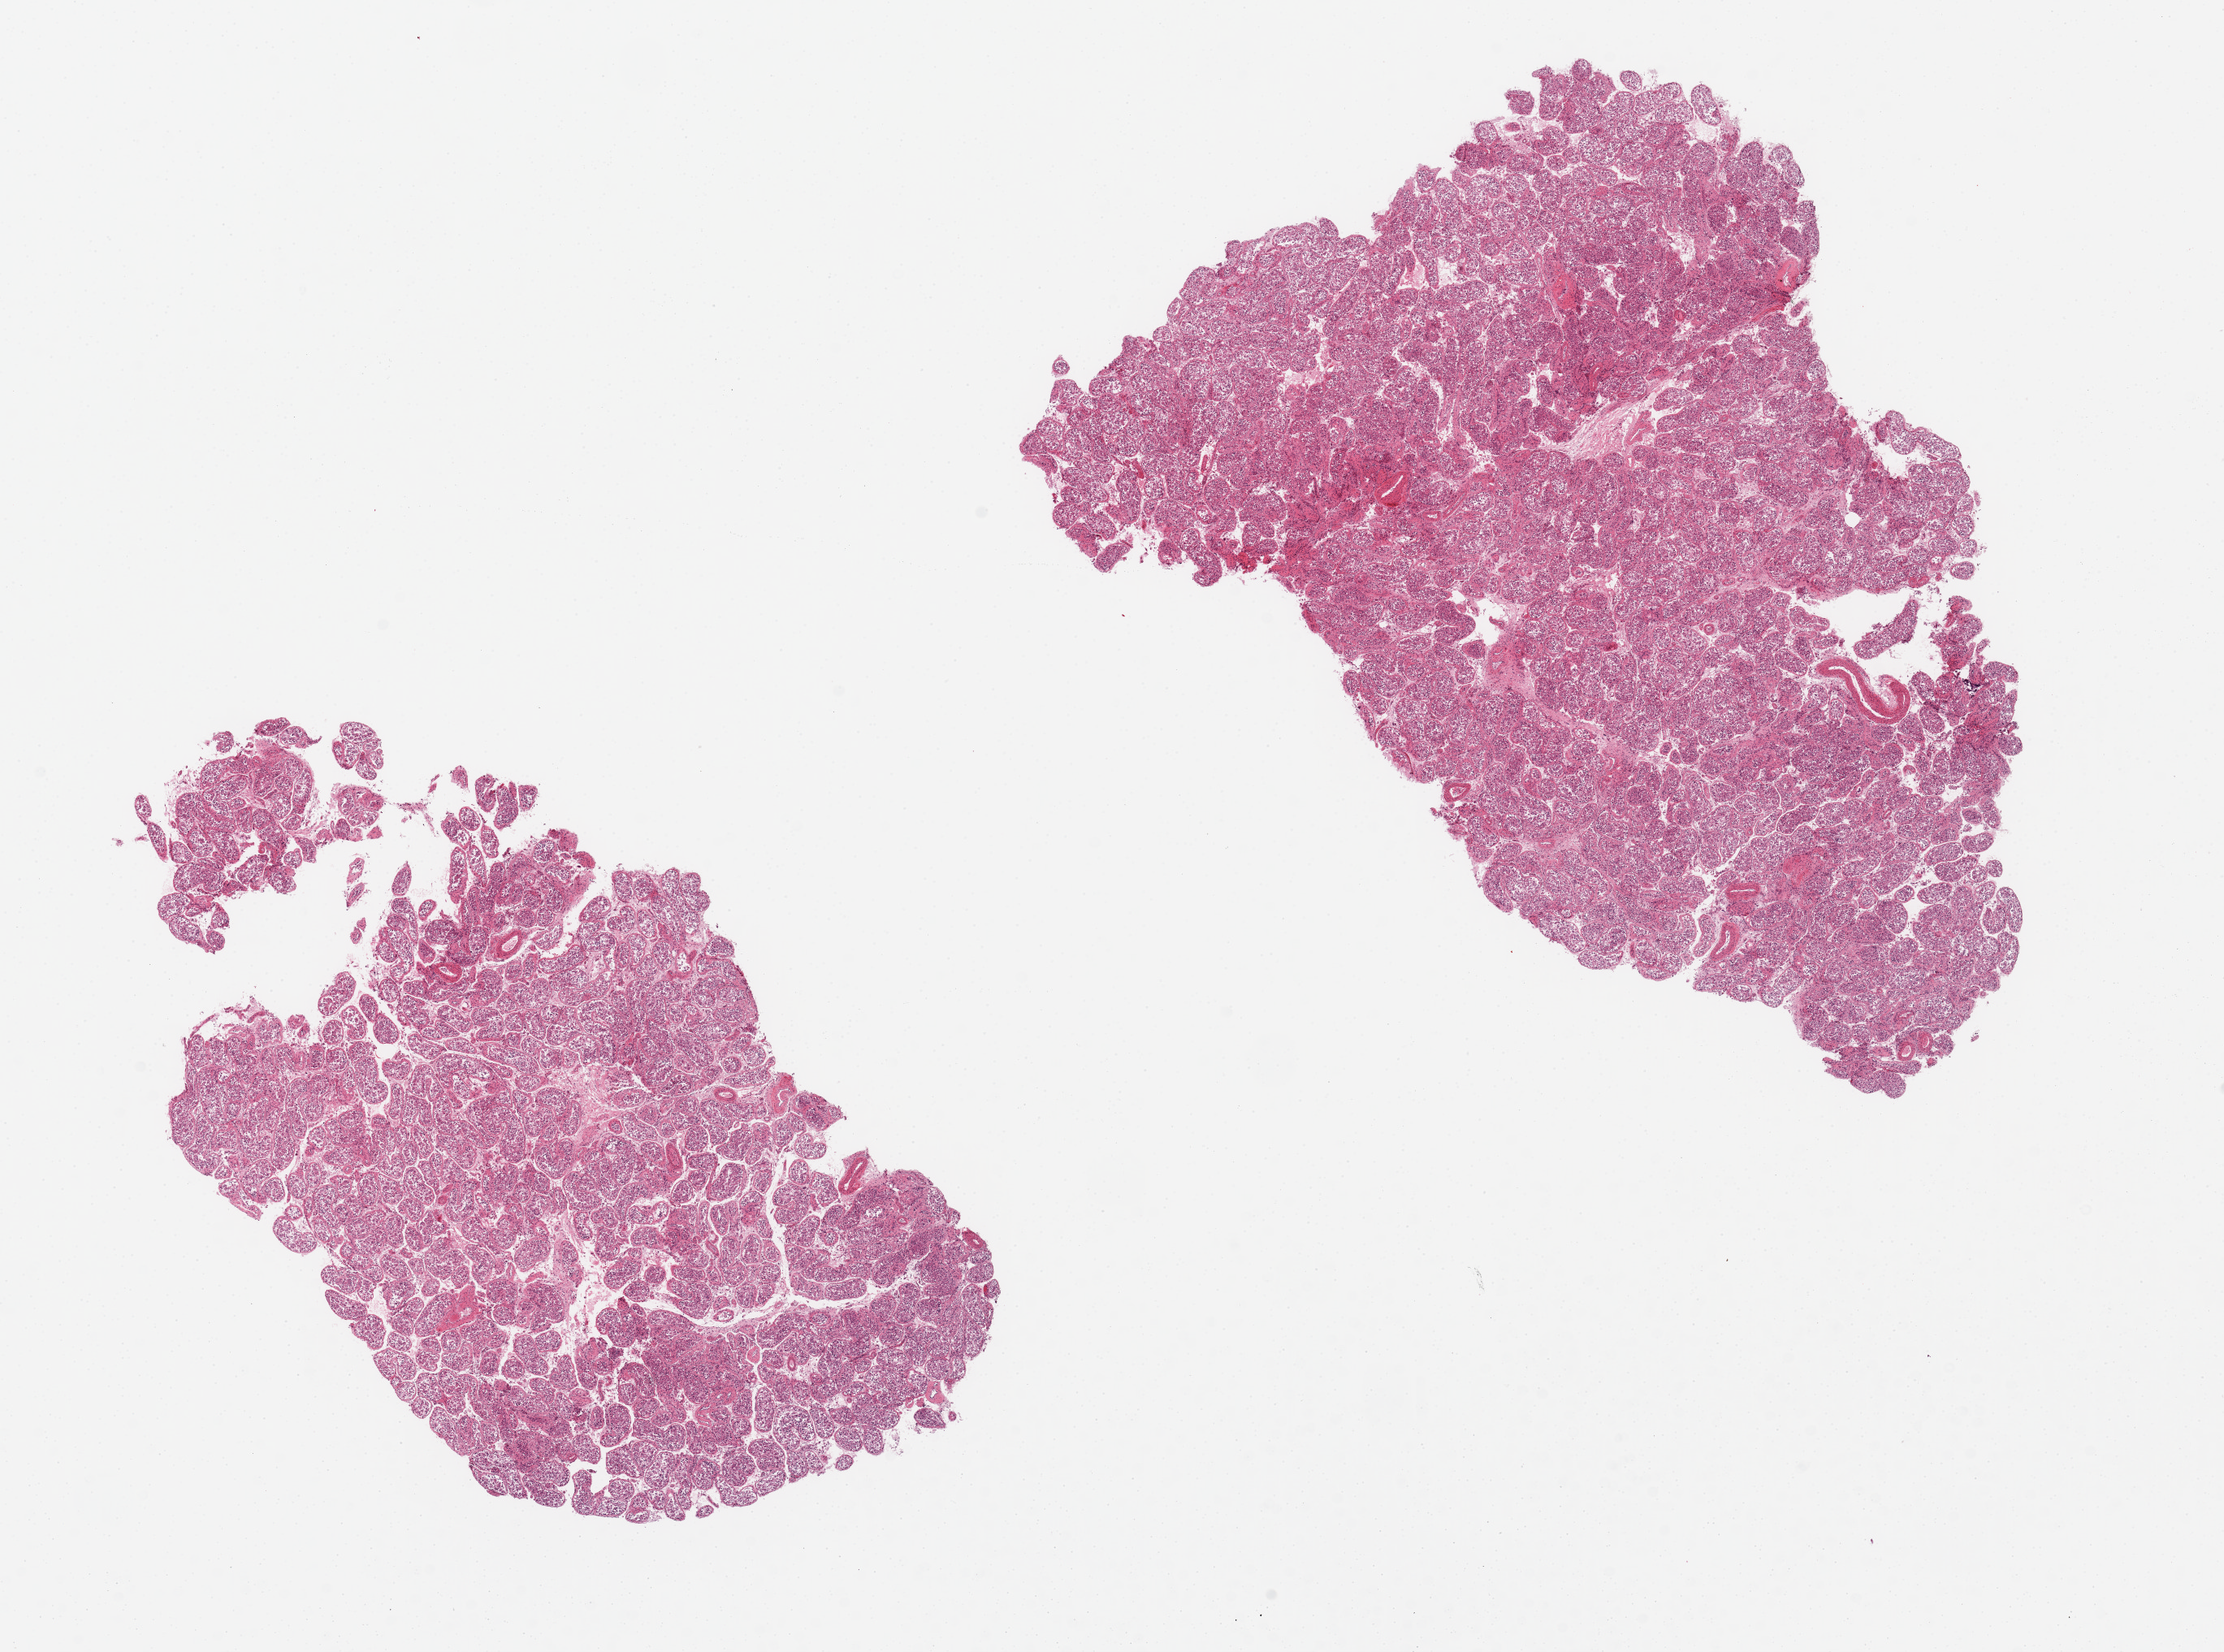
Digitized hematoxylin and eosin (H&E)-stained section, a low-resolution overview of the entire scanned area, about 21.7 x 16.1 mm, PAXgene-fixed paraffin-embedded (PFPE) section, section of testis (target tissue), donor tissue sample.
Pathologist's review note for this sample: 2 pieces, spermatogenesis present, moderately-severely autolzyed.